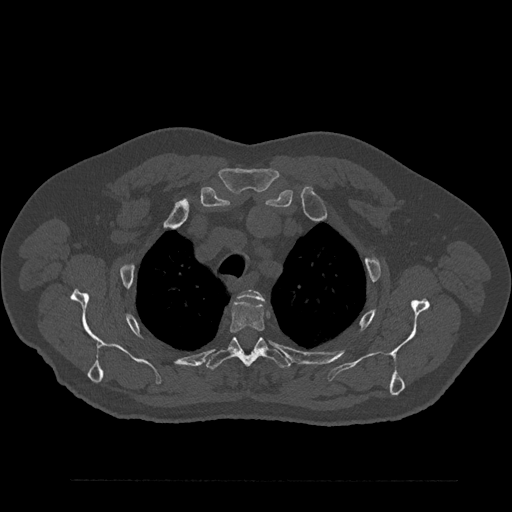
CT including the spine, one axial slice; position 668 of 797 along the scan axis; reconstruction kernel Br40s/3; 120 kVp; bone window (W 1800 / L 400 HU); 0.5 mm slice thickness; 512 × 512 image matrix, field of view 430 × 430 mm. Male patient, age 61 years. Case-level facts recorded for this patient, not image findings: primary cancer: prostate.
Outlined on this slice (semi-automatically segmented with operator editing):
- T2 vertebra: bounding box (x1, y1, x2, y2) in pixels: (239, 290, 264, 301)
- T3 vertebra: (229, 300, 265, 333)
- T4 vertebra: (207, 337, 290, 370)